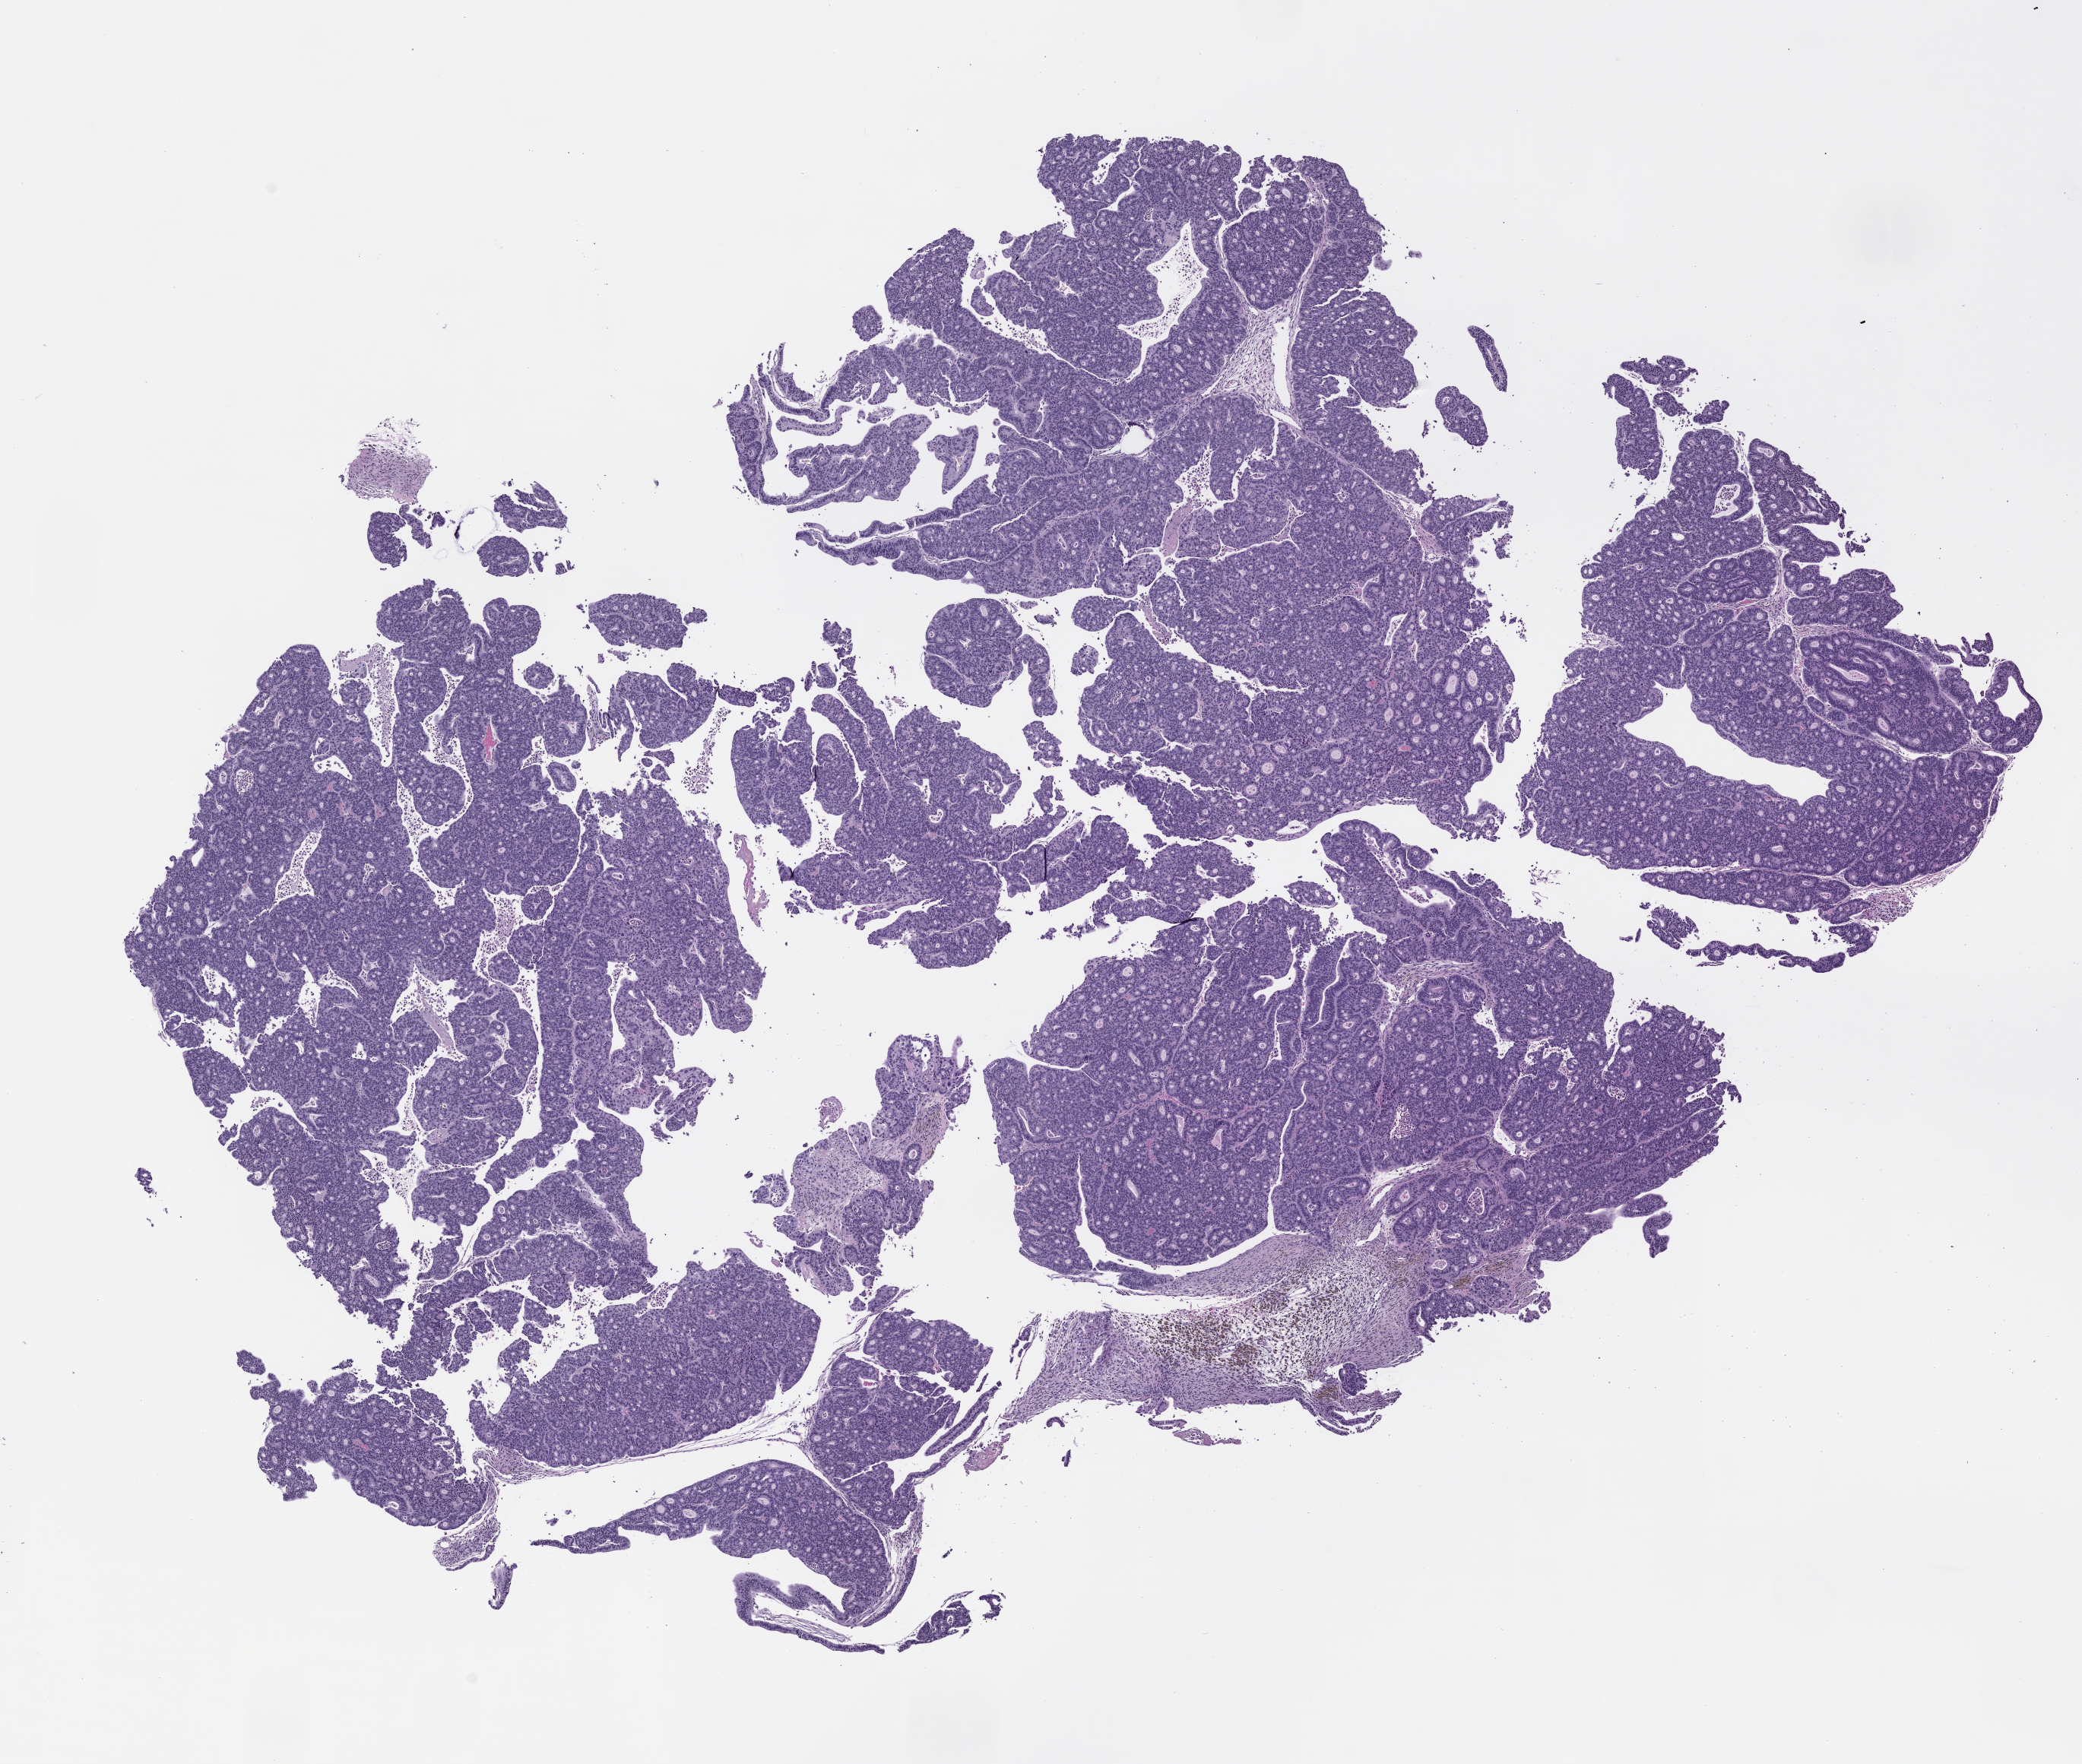
Whole-slide image, H&E: patient-derived xenograft (human tumor grown in a mouse), passage 2 — a low-resolution overview of the entire scanned area, about 11.0 x 9.3 mm, FFPE section, originating tumor site category: colon.
Originating patient diagnosis: Colon Adenocarcinoma.